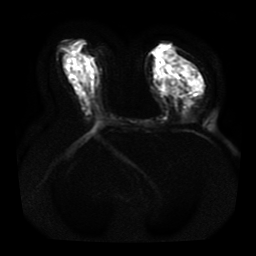
Breast MRI, one axial slice; slice 23 of 41 in the series (ordered by position); diffusion-weighted series; image 2 of 4 stored at this slice position (different b-values; order by instance number); 1.5 T; 5 mm slice thickness; 256 × 256 image matrix, field of view 330 × 330 mm. Female patient.
Outlined on this slice (manually delineated by an expert):
- tumour on diffusion-weighted imaging: bounding box [x1, y1, x2, y2] px = [177, 71, 201, 95]